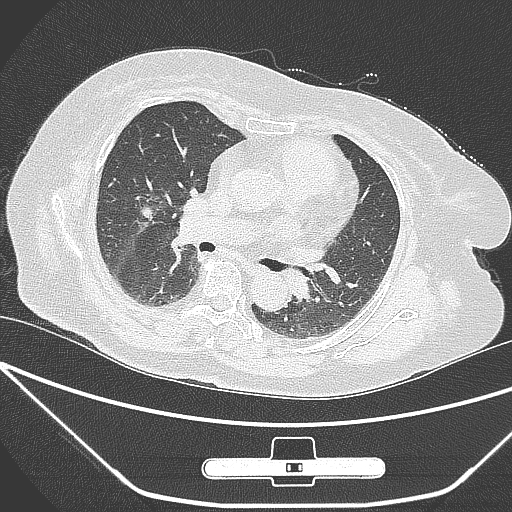
Chest CT, one axial slice. Position 152 of 245 along the scan axis. Lung window (W 1500 / L -600 HU). 1 mm slice thickness. 512 × 512 image matrix. Patient: female, 65 years. From the clinical record (not read from this slice): clinical TNM (as recorded): T1c N0 M0; histopathological grade: G3.
Structures marked on this image (rectangle marked by the reading radiologist):
- lung tumour (recorded histology: adenocarcinoma): box from (x=128, y=197) to (x=163, y=239) px